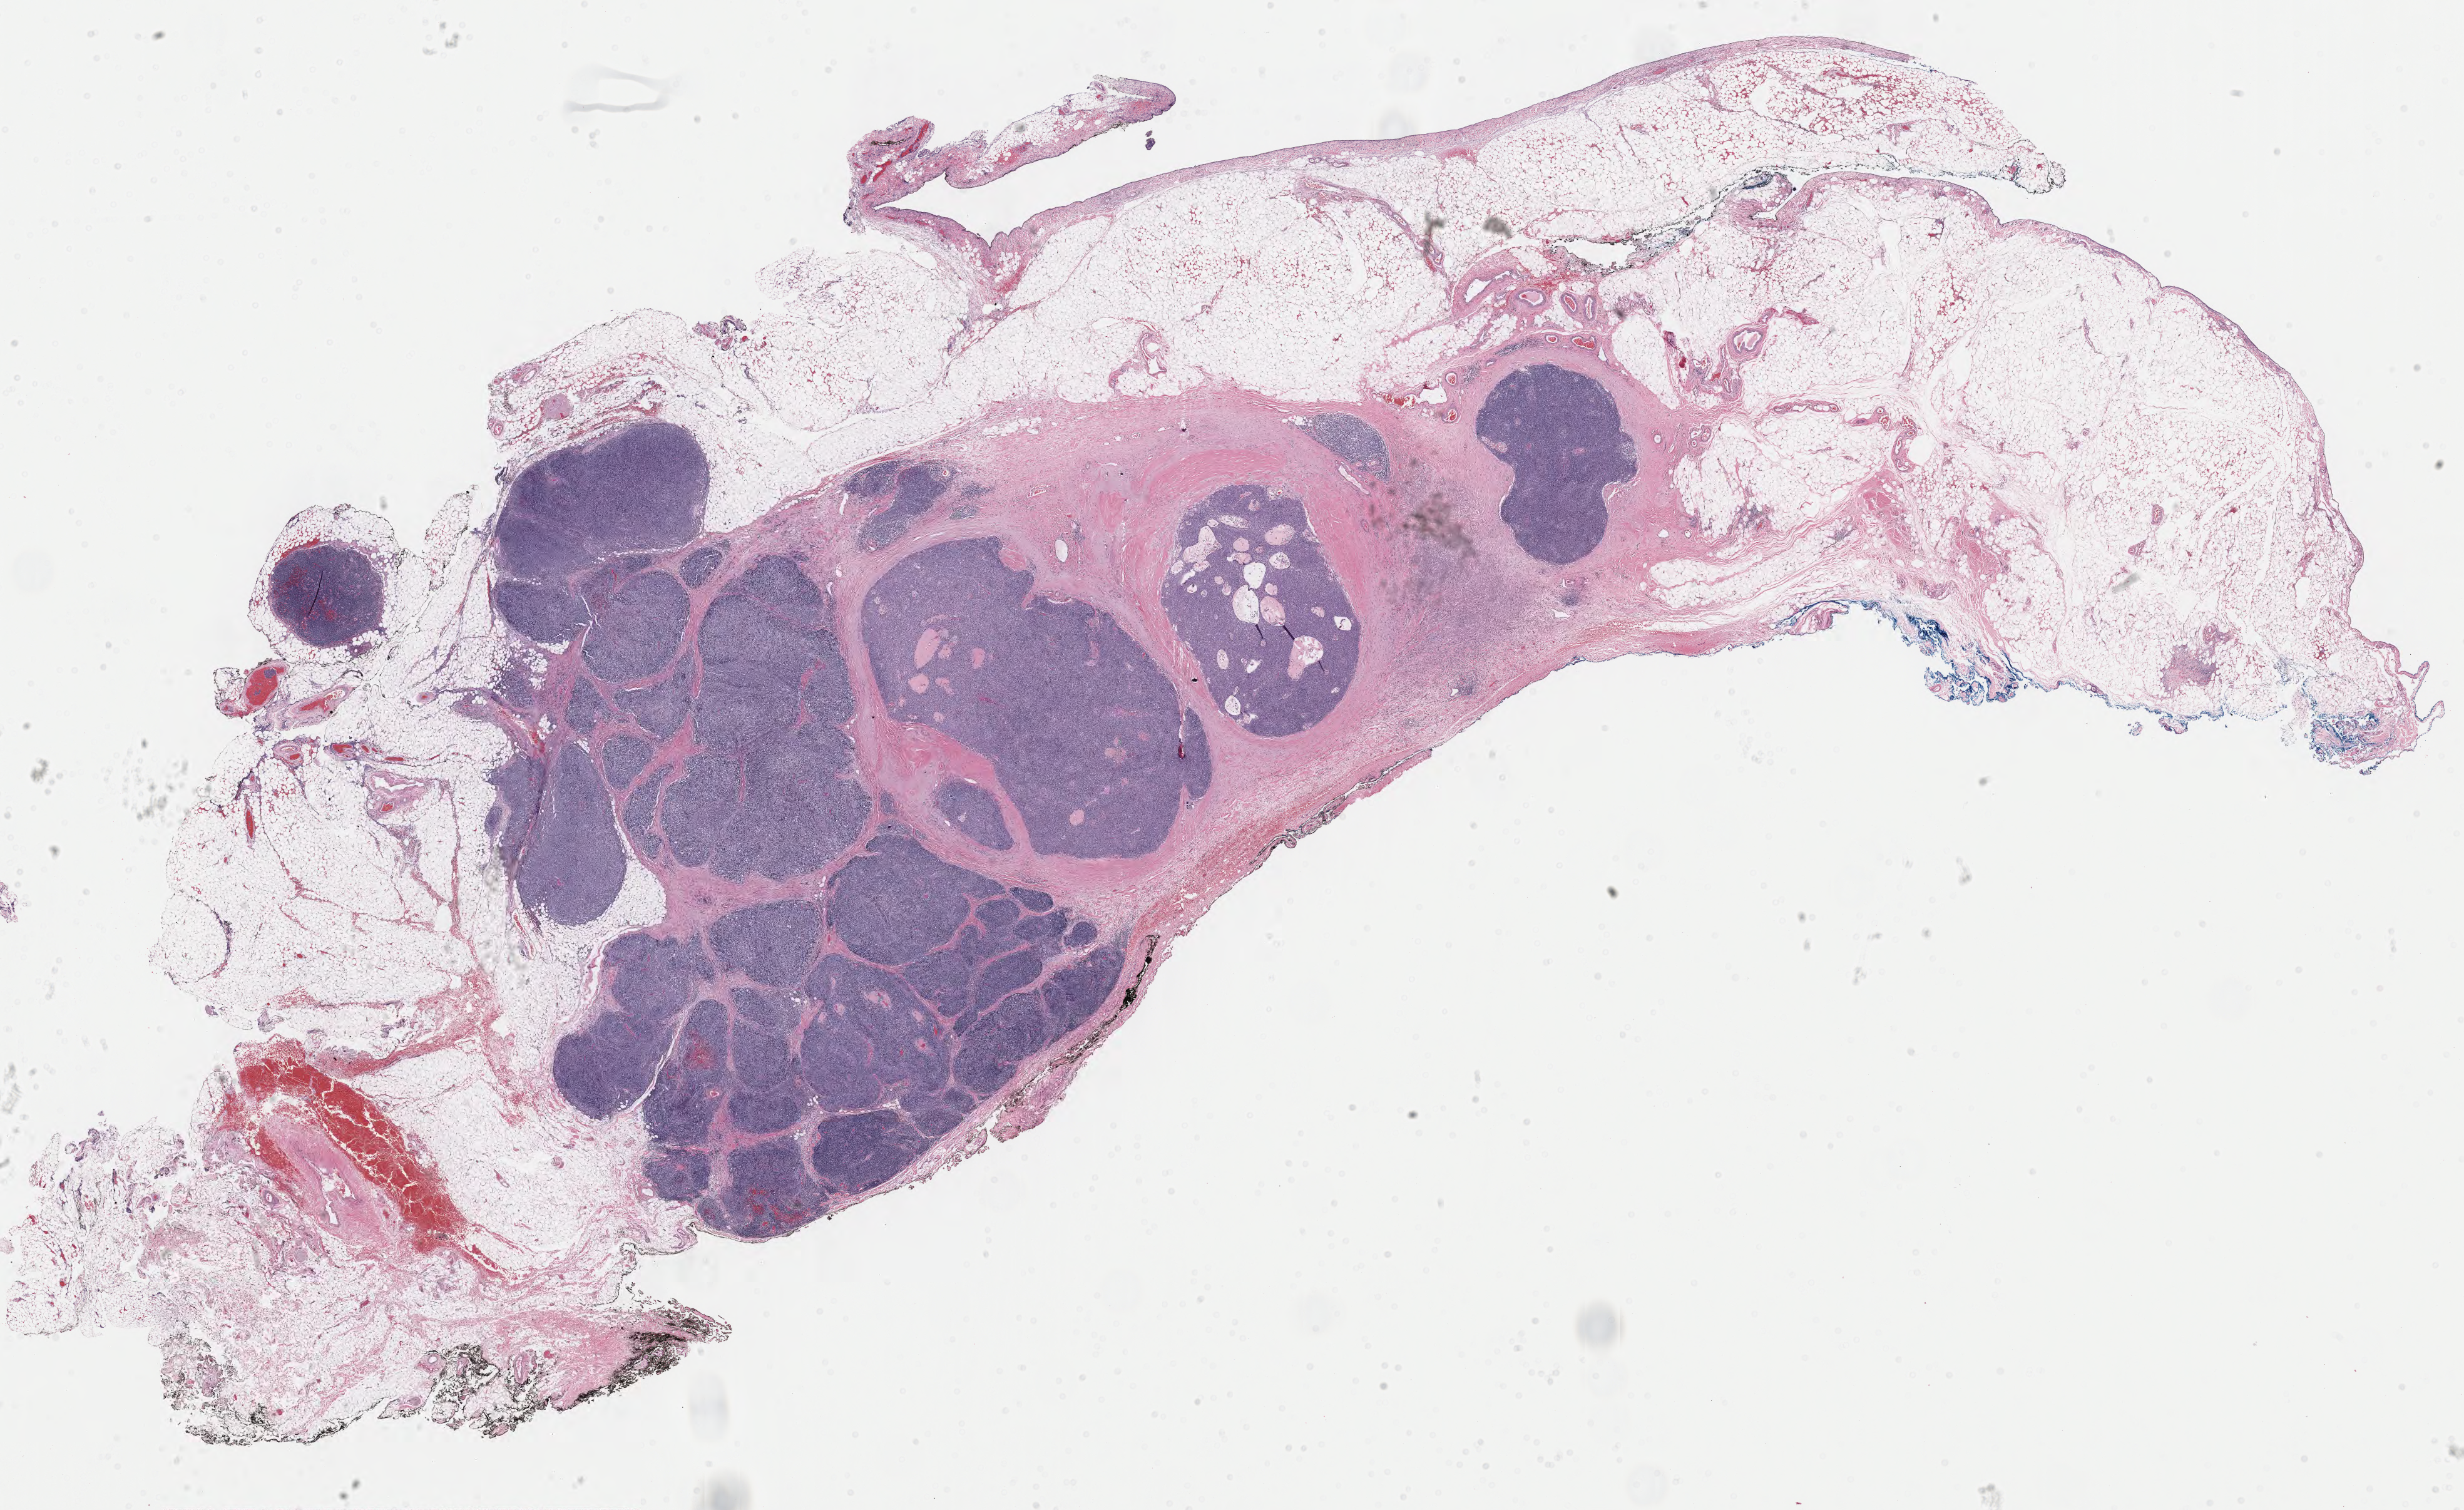
Digitized H&E-stained tissue section (whole slide), a low-resolution overview of the entire scanned area, about 31.2 x 19.1 mm; FFPE section; primary tumour sample from the thymus. Female patient; age at initial diagnosis 43 years.
Diagnosis: Thymoma, type B2, malignant.